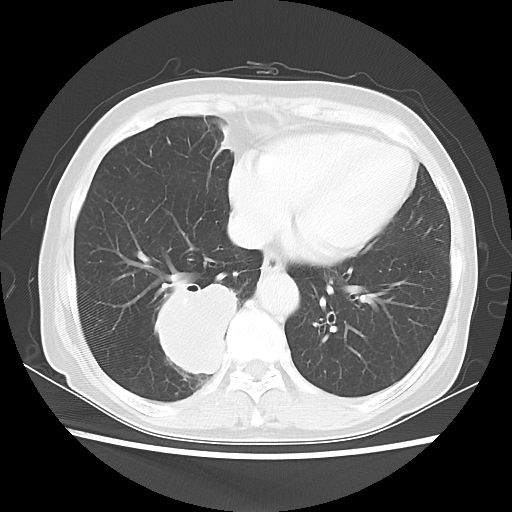
Chest CT, one axial slice. Slice 18 of 56 in the series (ordered by position). Reconstruction kernel LUNG. 120 kVp. Lung window (W 1500 / L -600 HU). 5 mm slice thickness. 512 × 512 image matrix, field of view 332 × 332 mm. Female patient, age 66 years. From the clinical record (not read from this slice): clinical TNM (as recorded): T2 N3 M0; histopathological grade: G3.
Outlined on this slice (bounding box drawn by a radiologist):
- lung tumour (recorded histology: small cell carcinoma): bounding box [x1, y1, x2, y2] px = [137, 261, 251, 387]